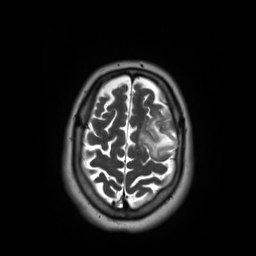
Brain MRI from a brain-tumour surgery series, one axial slice. Slice 46 of 59 in the series (ordered by position). 256 × 256 image matrix, field of view 250 × 250 mm. From the clinical record (not read from this slice): histopathology: Oligodendroglioma; WHO grade: 2; IDH mutation: yes.
Annotated regions visible in this slice (outlined manually by an expert reader):
- tumour: box from (x=139, y=111) to (x=180, y=158) px